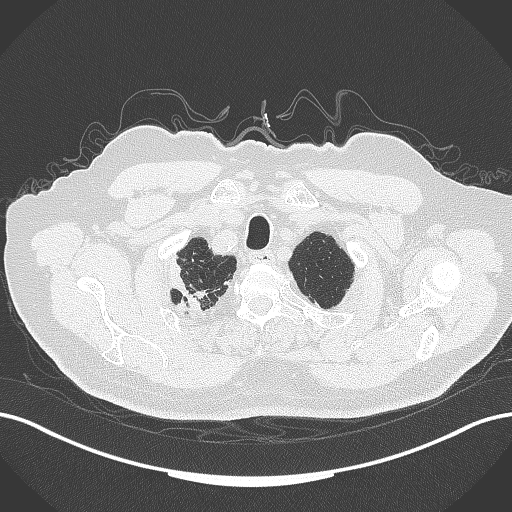
Chest CT, one axial slice; slice 330 of 389 in the series (ordered by position); reconstruction kernel B70f; 120 kVp; lung window (W 1500 / L -600 HU); 1 mm slice thickness; 512 × 512 image matrix. Patient: male, 72 years. Case-level facts recorded for this patient, not image findings: clinical TNM (as recorded): T1a N0 M0.
Annotated regions visible in this slice (bounding box drawn by a radiologist):
- lung tumour (recorded histology: squamous cell carcinoma): bounding box [x1, y1, x2, y2] px = [163, 256, 204, 318]